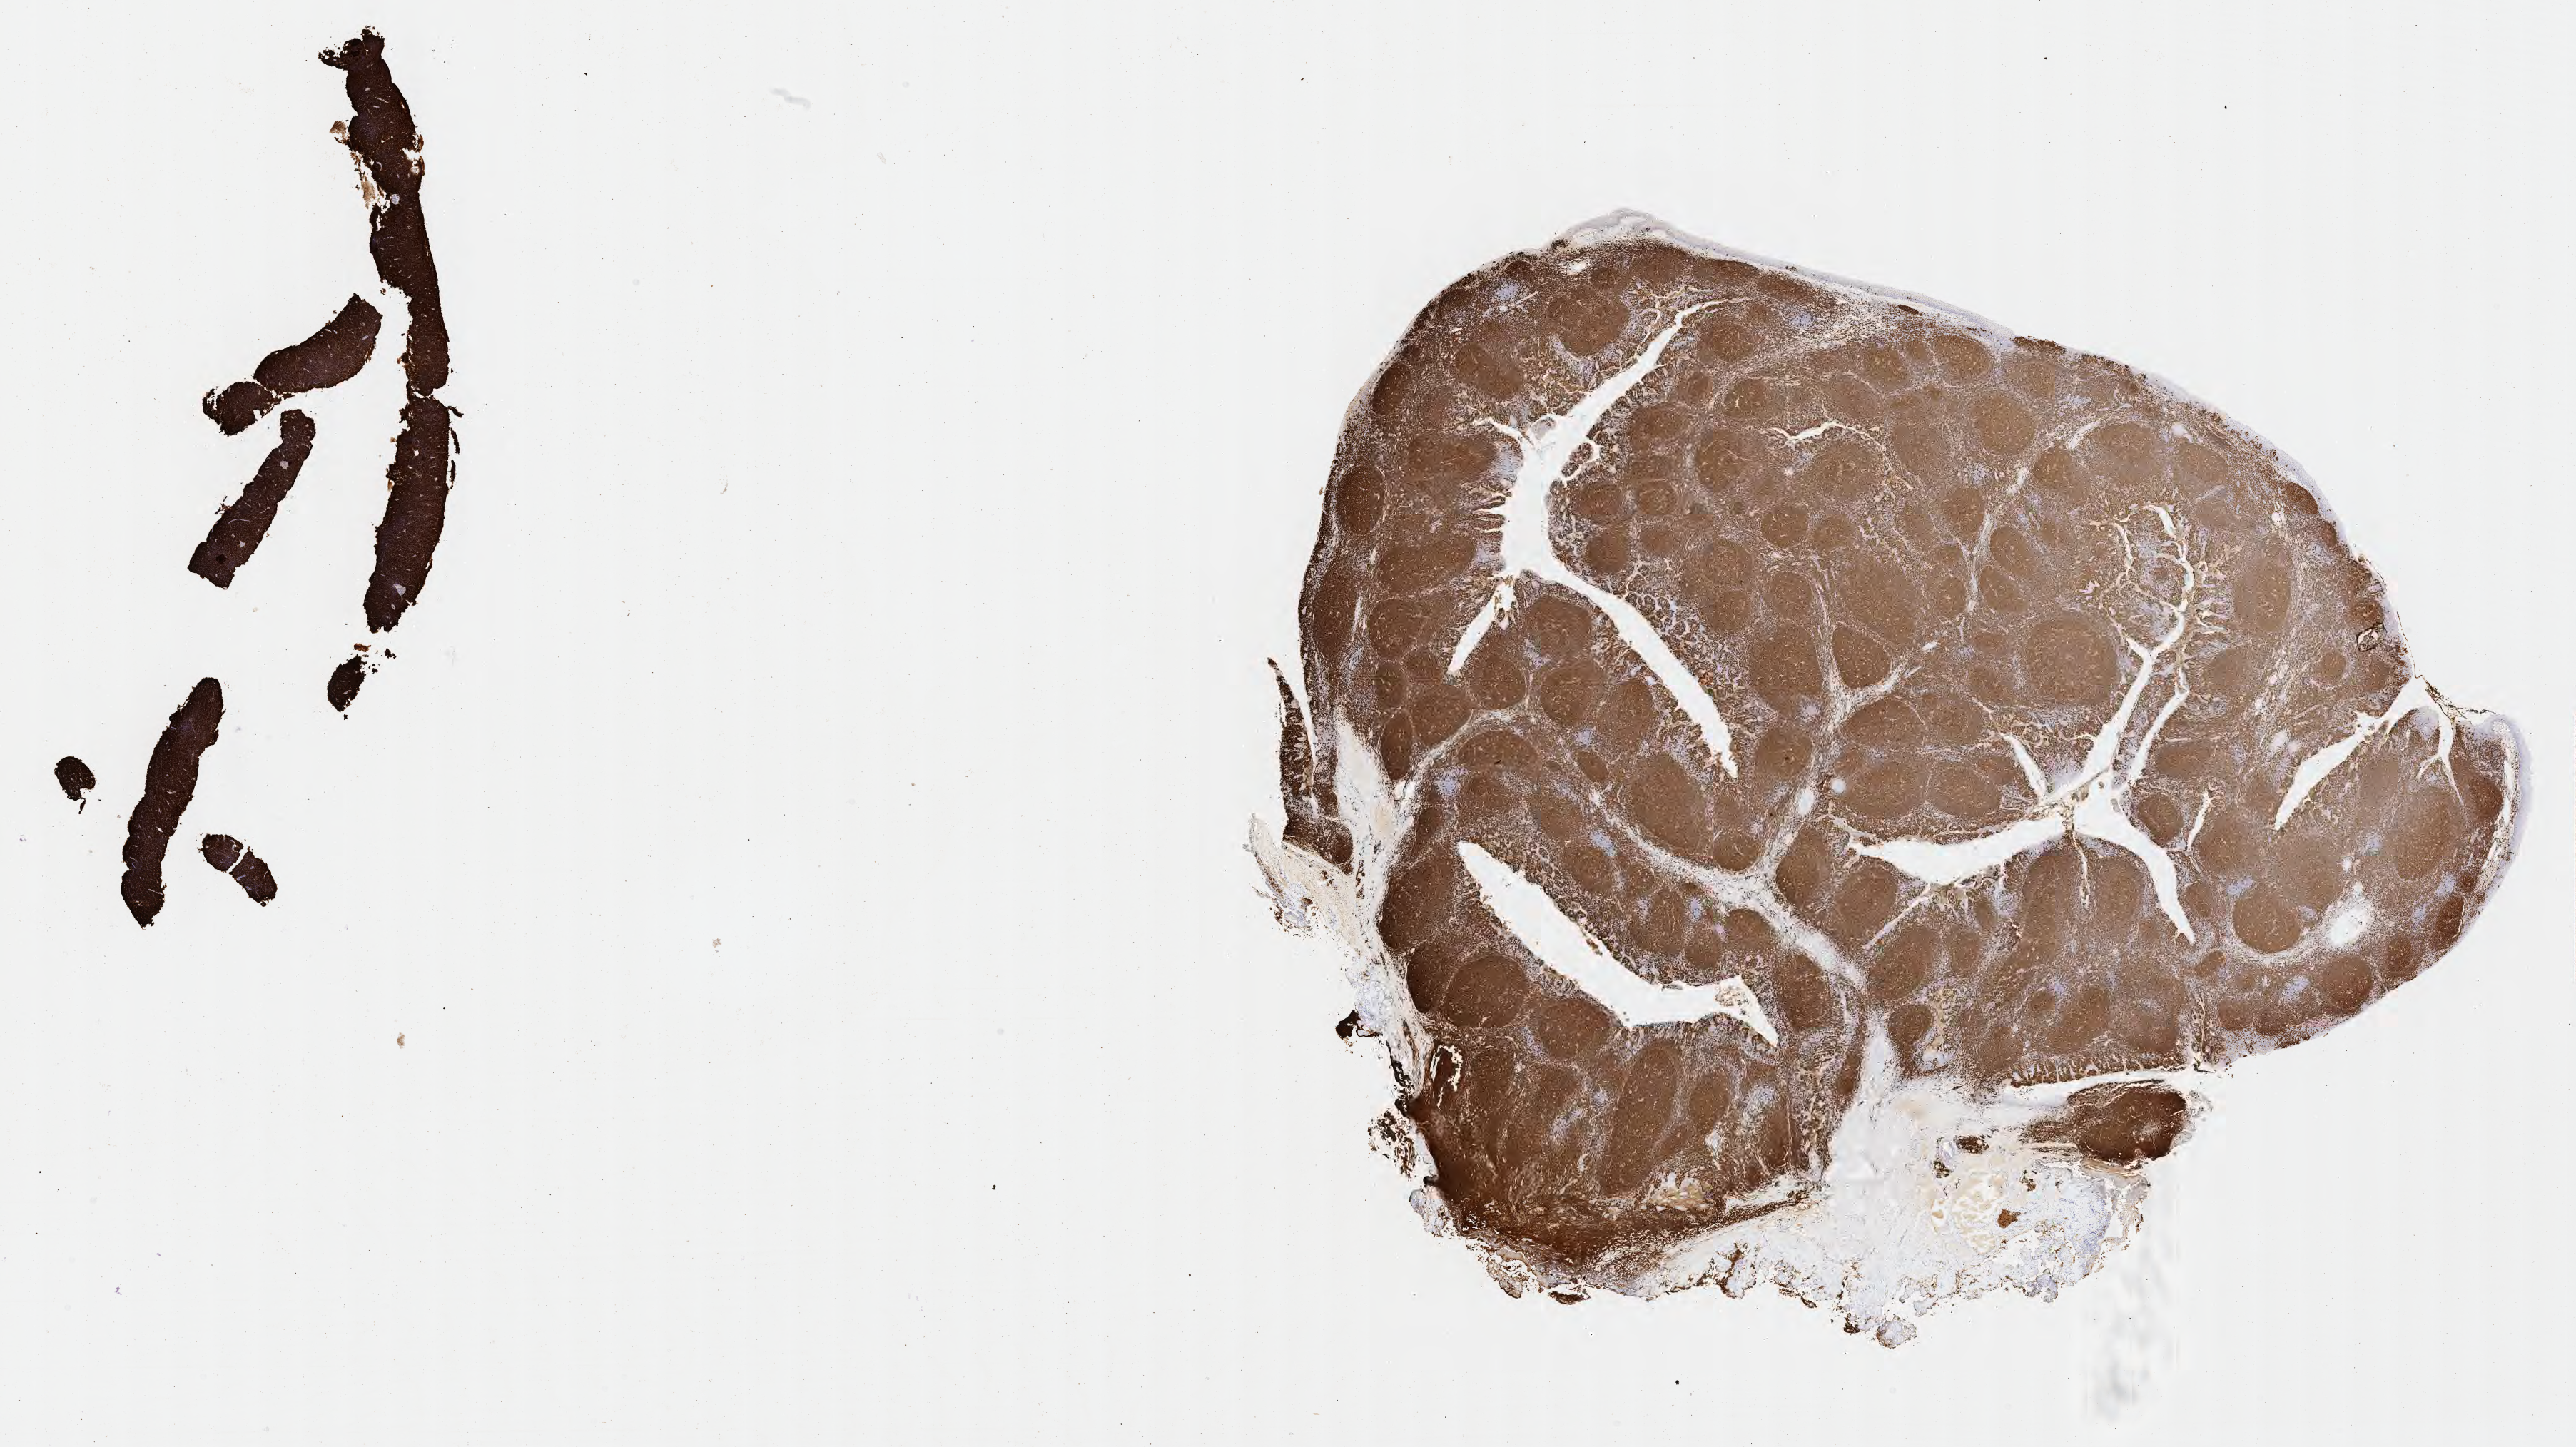
Immunohistochemistry (IHC) whole-slide image stained for CD20, low-resolution overview of the scanned area, about 29.2 x 16.4 mm. Tumor tissue. Male patient; age at initial diagnosis 8 years.
Diagnosis: Burkitt lymphoma, NOS.